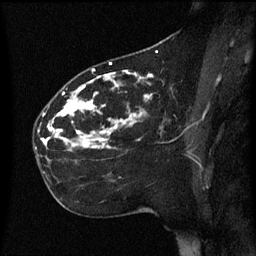
Breast MRI (dynamic contrast-enhanced), one sagittal slice. Slice 33 of 60 in the series (ordered by position). Dynamic contrast-enhanced series, image 2 of 3 at this slice position (ordered by acquisition). 1.5 T. TE 4.2 ms, TR 8.4 ms. 256 × 256 image matrix. Patient: female, 35 years. Case-level facts recorded for this patient, not image findings: setting: breast cancer imaged before/during neoadjuvant chemotherapy; receptor status: HER2-positive.
Annotated regions visible in this slice (semi-automatic segmentation, software-assisted and operator-edited):
- analysis volume of interest (the breast-tissue region the enhancement analysis was run in; not a lesion): box from (x=34, y=78) to (x=173, y=163) px
- tumour enhancement mask (voxels above the 70 % enhancement threshold inside the analysis volume of interest): (x=42, y=78)–(x=150, y=149)